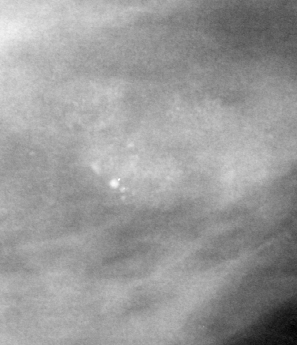
Crop from a digitized film mammogram around one marked abnormality, left breast, MLO view, BI-RADS breast density category 3 (scale 1–4).
Marked abnormality: calcifications, morphology pleomorphic, distribution clustered; BI-RADS assessment category 4; subtlety rating 3 on a 1 (subtle) to 5 (obvious) scale; pathology result (as recorded, not read from the image): benign.